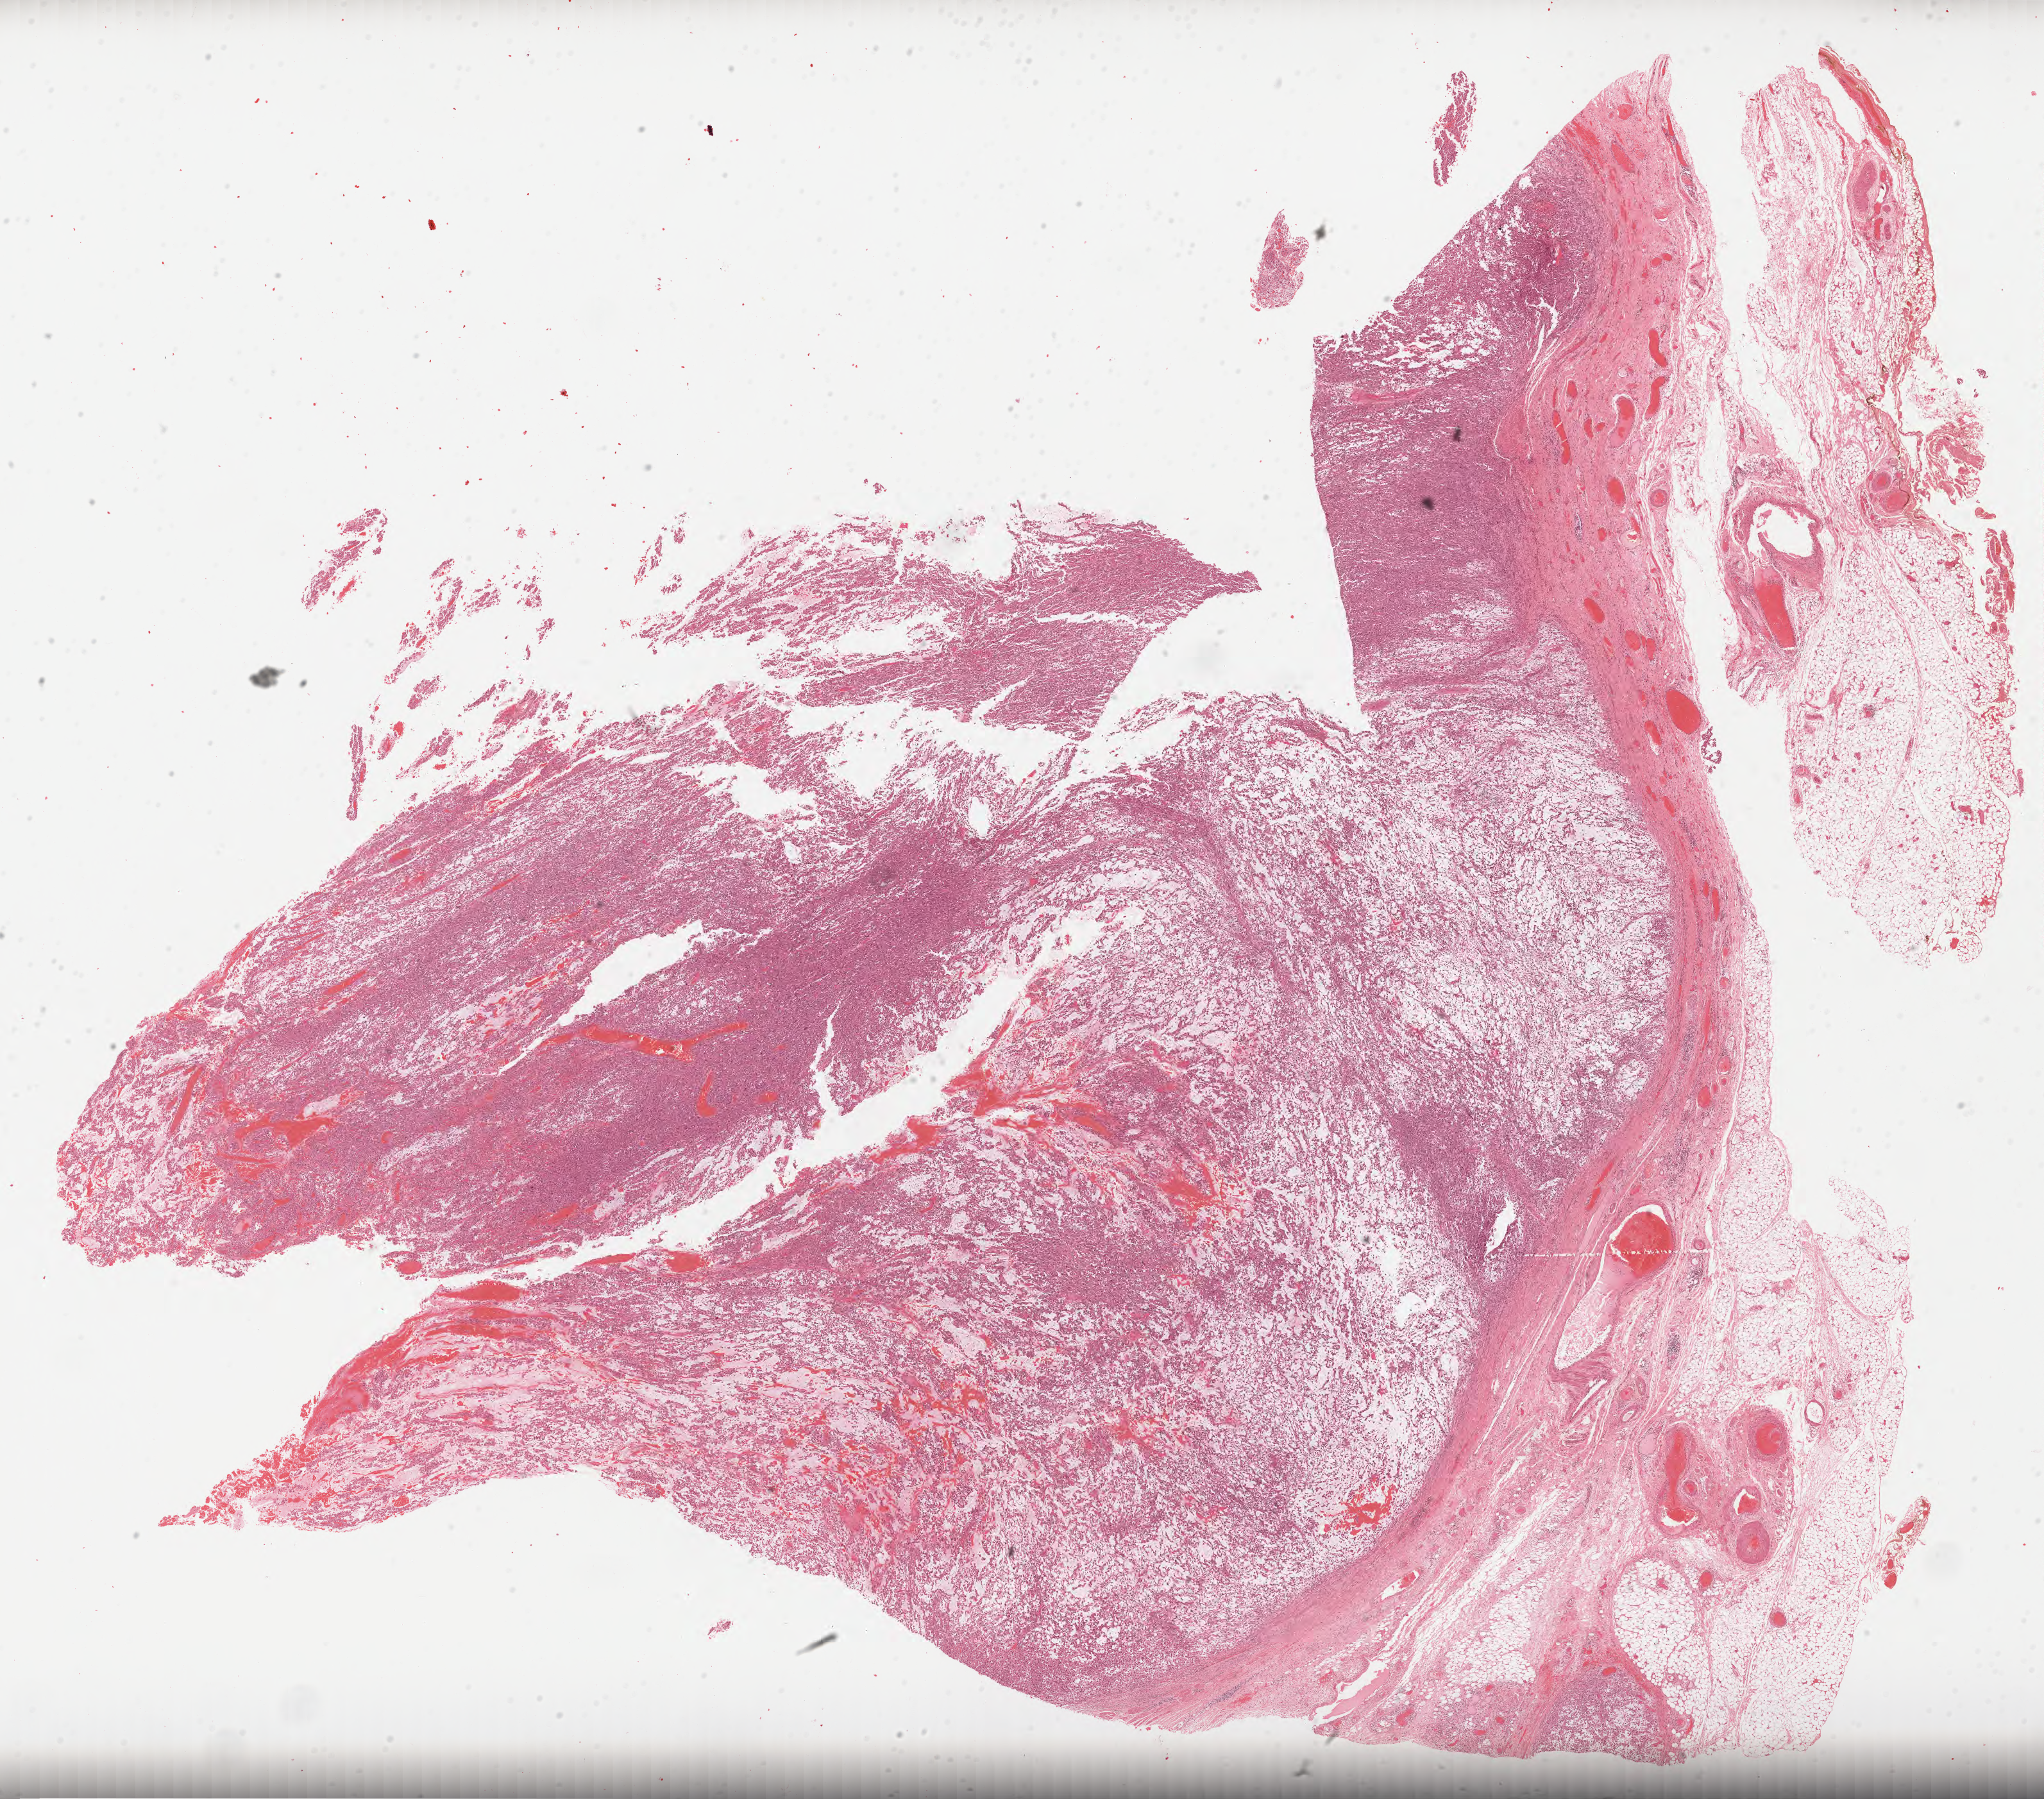
Digitized H&E-stained tissue section (whole slide) — shown as a low-resolution overview of the whole scanned area (about 25.7 x 22.6 mm); formalin-fixed paraffin-embedded (FFPE) diagnostic section; primary tumour sample from the esophagus. Male, age 49 years at initial diagnosis. Histologic grade: G3 (poorly differentiated).
AJCC pathologic stage: III (6th edition). Lymph nodes positive (case pathology): 8 of 35 examined. Histologic diagnosis: Squamous cell carcinoma, NOS (lower third of esophagus). TNM: T3 N1 M0.